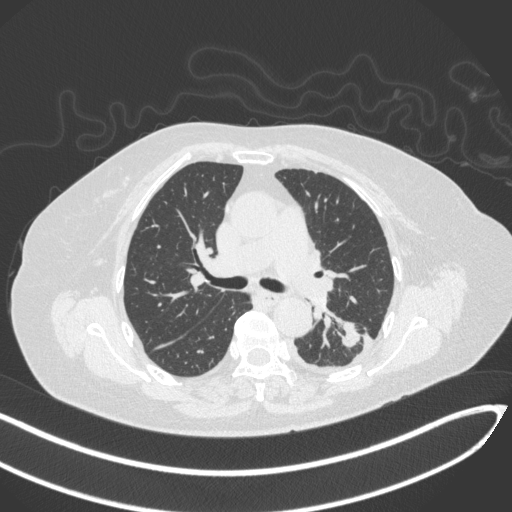
Chest CT, one axial slice. Position 196 of 270 along the scan axis. Lung window (W 1500 / L -600 HU). 1 mm slice thickness. 512 × 512 image matrix. Female patient, age 76 years. Case-level facts recorded for this patient, not image findings: clinical TNM (as recorded): T1c N0 M0.
Annotated regions visible in this slice (bounding box drawn by a radiologist):
- lung tumour (recorded histology: adenocarcinoma): box from (x=334, y=319) to (x=361, y=349) px